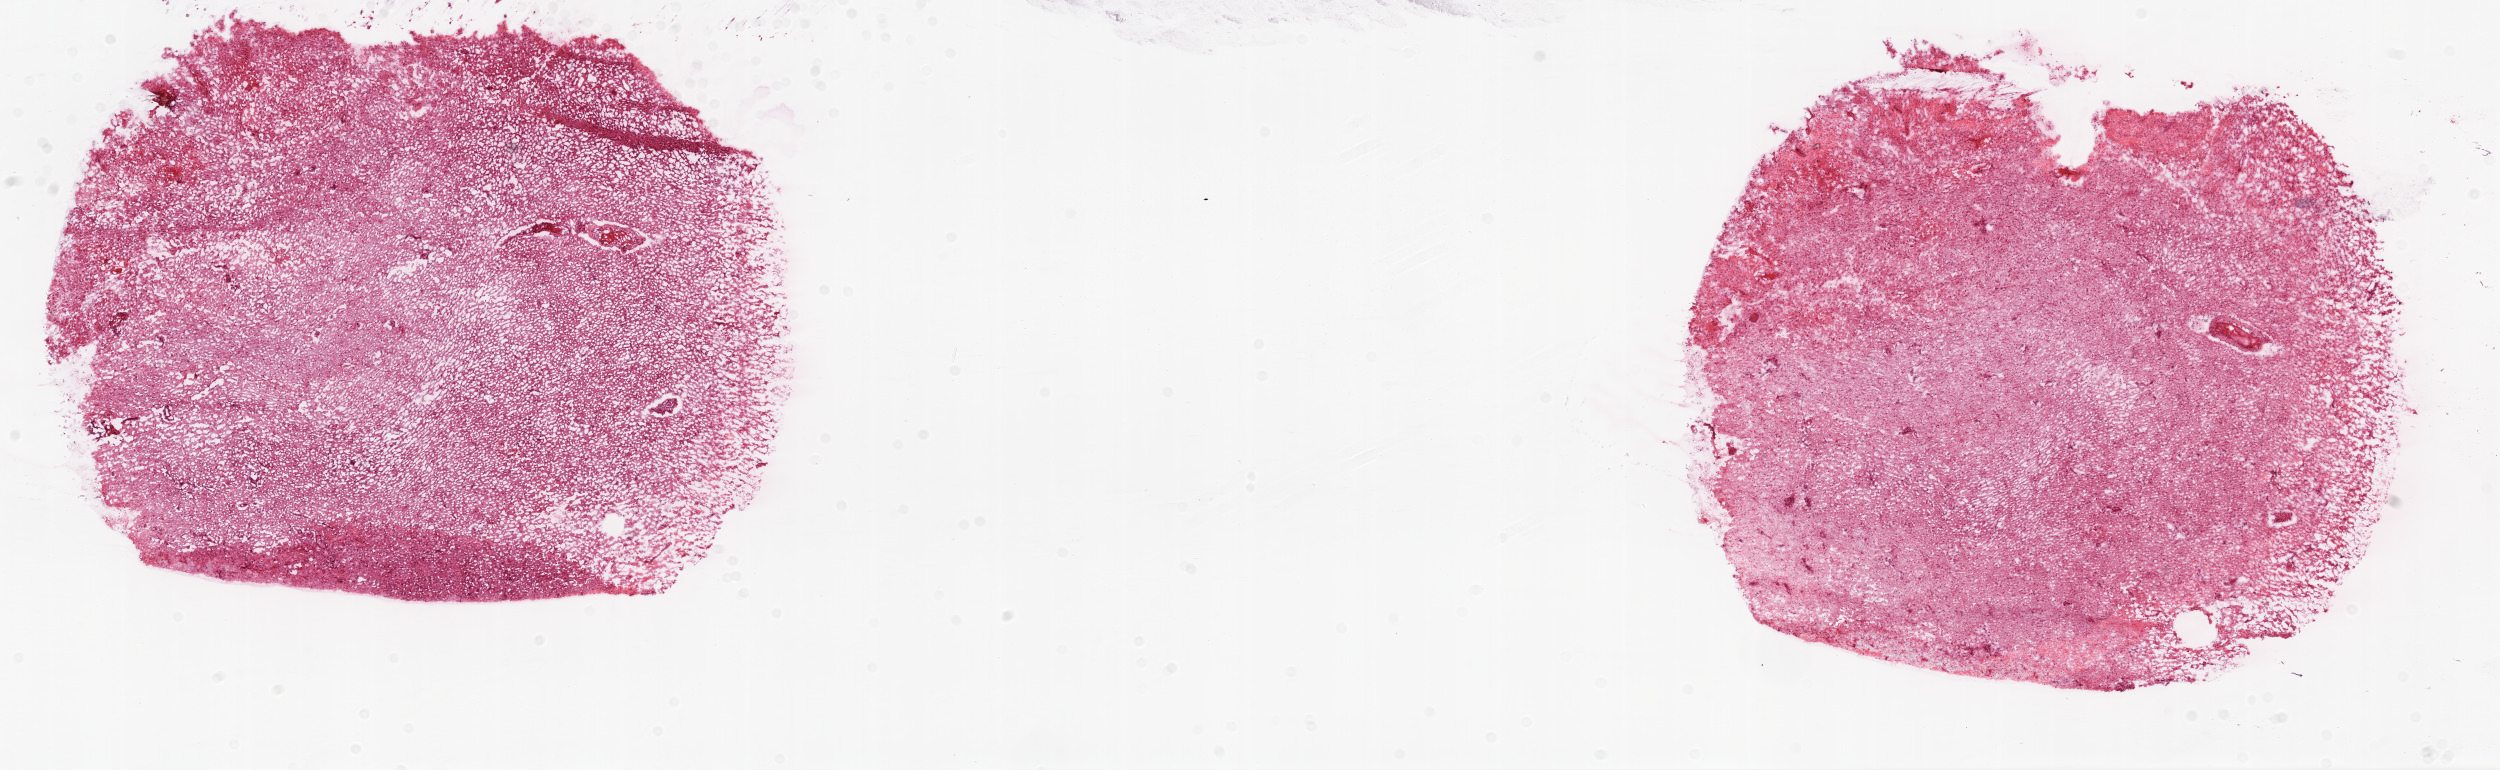
H&E-stained whole-slide image — low-resolution overview of the scanned area, about 20.1 x 6.2 mm (from a 20x scan); frozen section from the top of the tissue portion; primary tumour sample from the brain. Male, age 52 years at initial diagnosis.
Pathologic diagnosis: Glioblastoma.